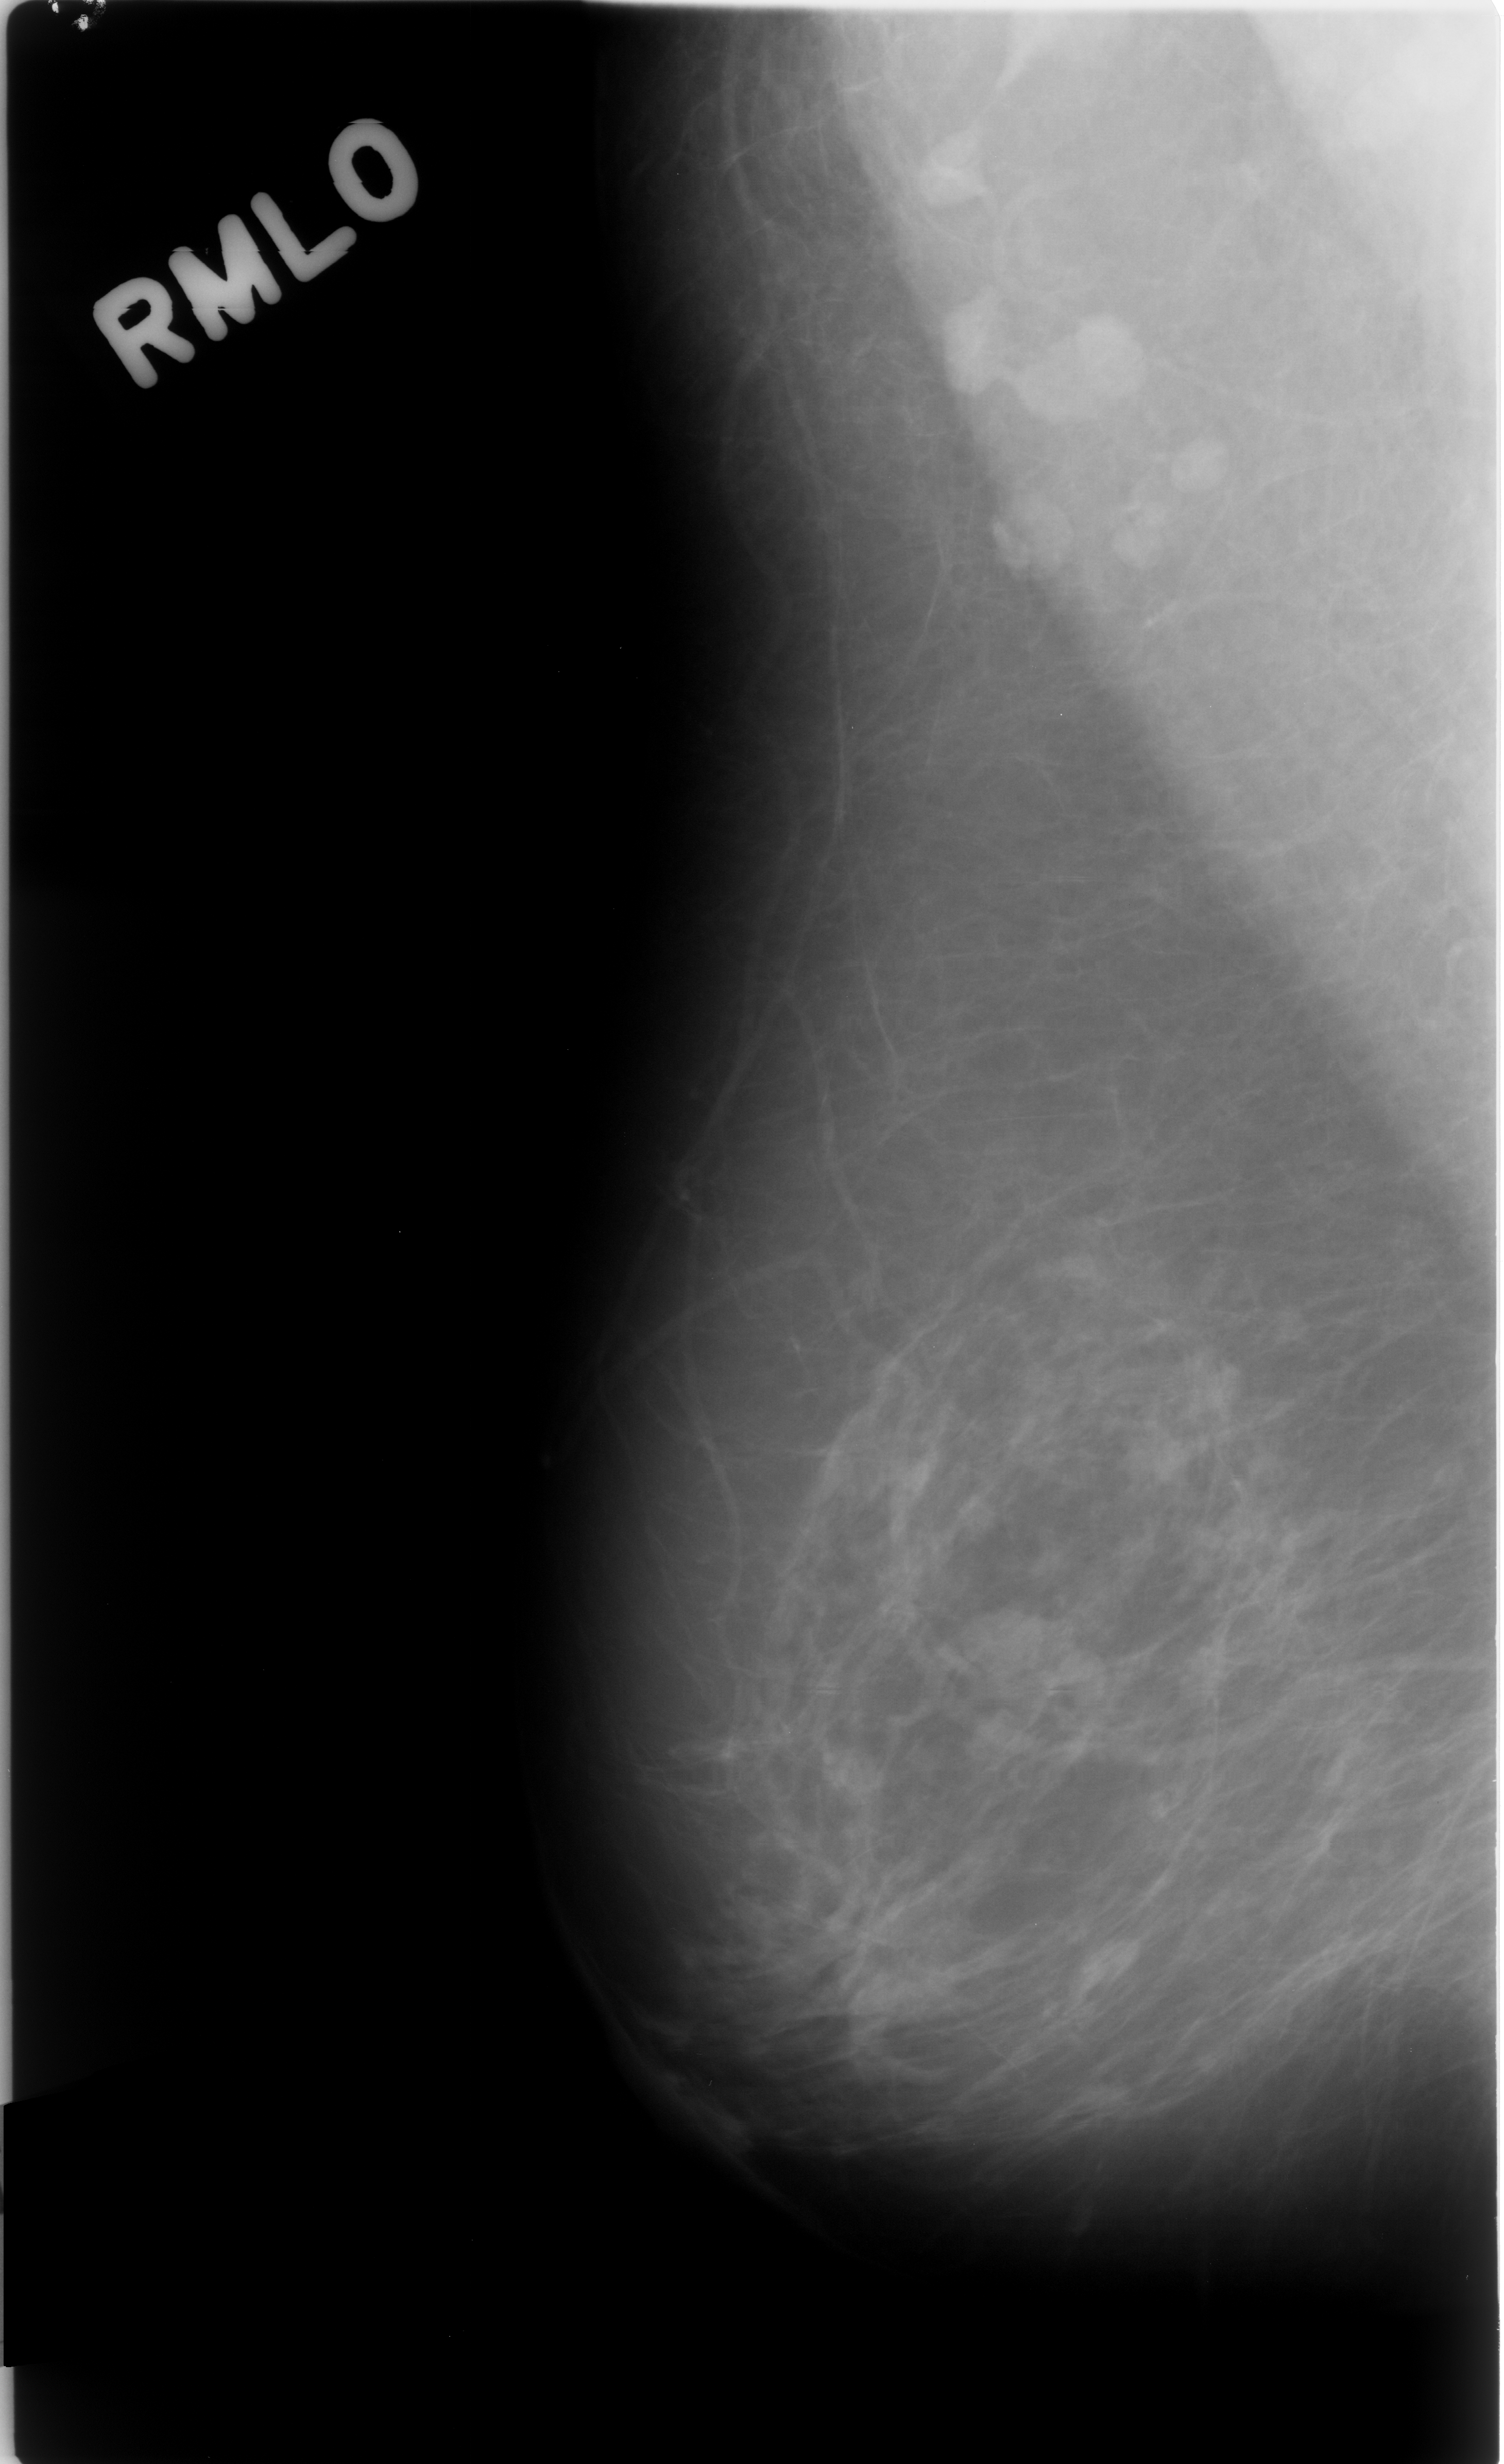
Mammogram (digitized film); right breast; mediolateral oblique (MLO) view; breast composition: almost entirely fatty (BI-RADS density category 1 of 4); 1504 × 2464 image matrix.
Marked abnormalities (boxes around the expert regions of interest):
- mass, shape lobulated, margins circumscribed; BI-RADS assessment category 3; outcome (as recorded, no biopsy): benign without callback (not worked up further): bounding box [x1, y1, x2, y2] px = [945, 1604, 1109, 1712]